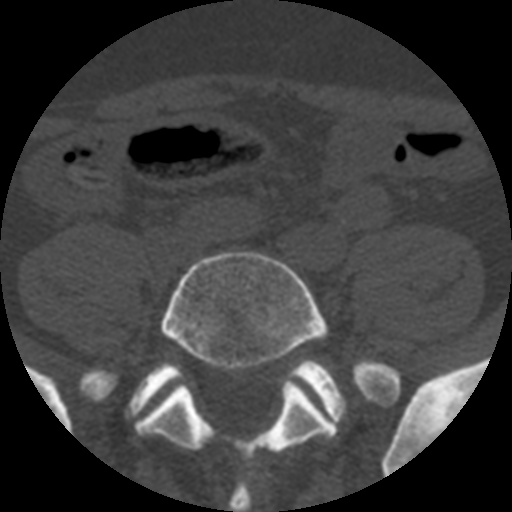
CT including the spine, one axial slice. Position 59 of 508 along the scan axis. Reconstruction kernel STANDARD. 120 kVp. Bone window (W 1800 / L 400 HU). 1.25 mm slice thickness. 512 × 512 image matrix. Patient age 57 years. Case-level facts recorded for this patient, not image findings: primary cancer: prostate.
Outlined on this slice (semi-automatically segmented with operator editing):
- L5 vertebra: bounding box (x1, y1, x2, y2) in pixels: (136, 252, 392, 467)